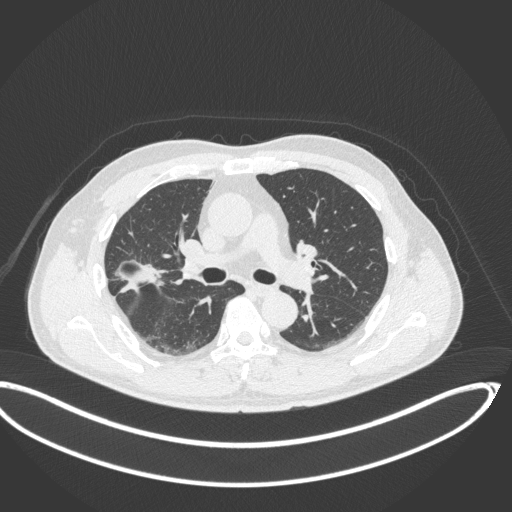
Chest CT, one axial slice. Position 206 of 341 along the scan axis. Reconstruction kernel B31f. 120 kVp. Lung window (W 1500 / L -600 HU). 1 mm slice thickness. 512 × 512 image matrix, field of view 439 × 439 mm. Male patient, age 63 years. From the clinical record (not read from this slice): clinical TNM (as recorded): T1c N0 M0; histopathological grade: G2-3.
Structures marked on this image (rectangle marked by the reading radiologist):
- lung tumour (recorded histology: adenocarcinoma): bounding box <115,257,166,296> (left, top, right, bottom; pixels)